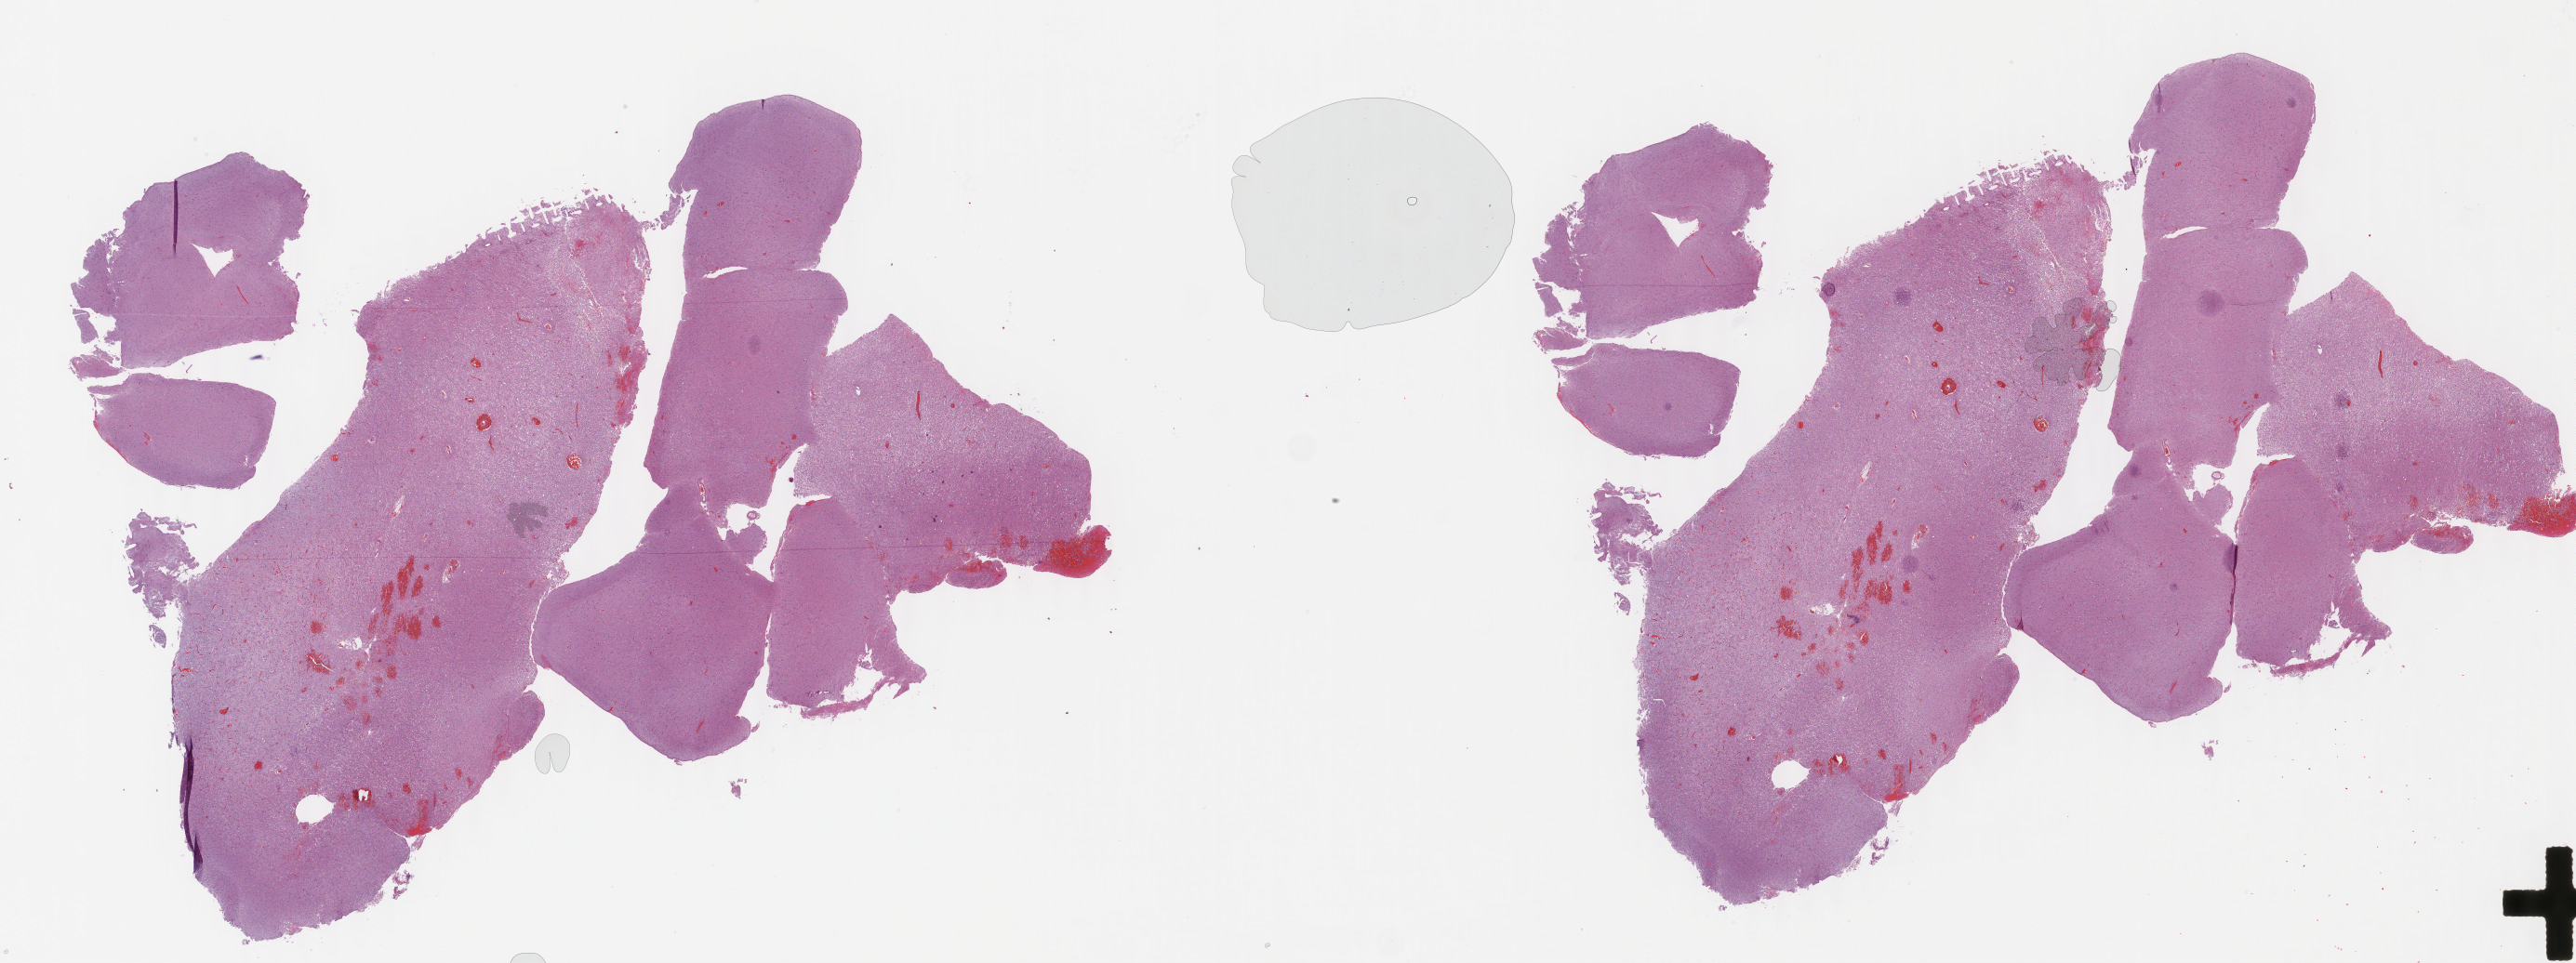
Digitized H&E tissue section (whole slide), shown as a low-resolution overview of the whole scanned area (about 44.8 x 16.7 mm, acquisition: 40x scan). Formalin-fixed paraffin-embedded (FFPE) diagnostic section. Sample: primary tumour, brain. Male patient; age at initial diagnosis 47 years. Histologic grade: G2 (moderately differentiated).
Laterality: right. Pathologic diagnosis: Oligodendroglioma, NOS (cerebrum).